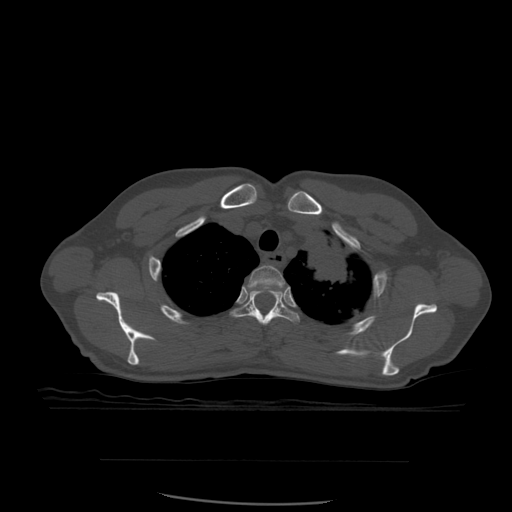
CT including the spine, one axial slice; position 446 of 574 along the scan axis; bone window (W 1800 / L 400 HU); 512 × 512 image matrix, field of view 392 × 392 mm. Patient age 48 years. Case-level facts recorded for this patient, not image findings: primary cancer: lung.
Outlined on this slice (semi-automatically segmented with operator editing):
- T2 vertebra: bounding box (x1, y1, x2, y2) in pixels: (248, 266, 285, 294)
- T3 vertebra: (231, 288, 300, 326)